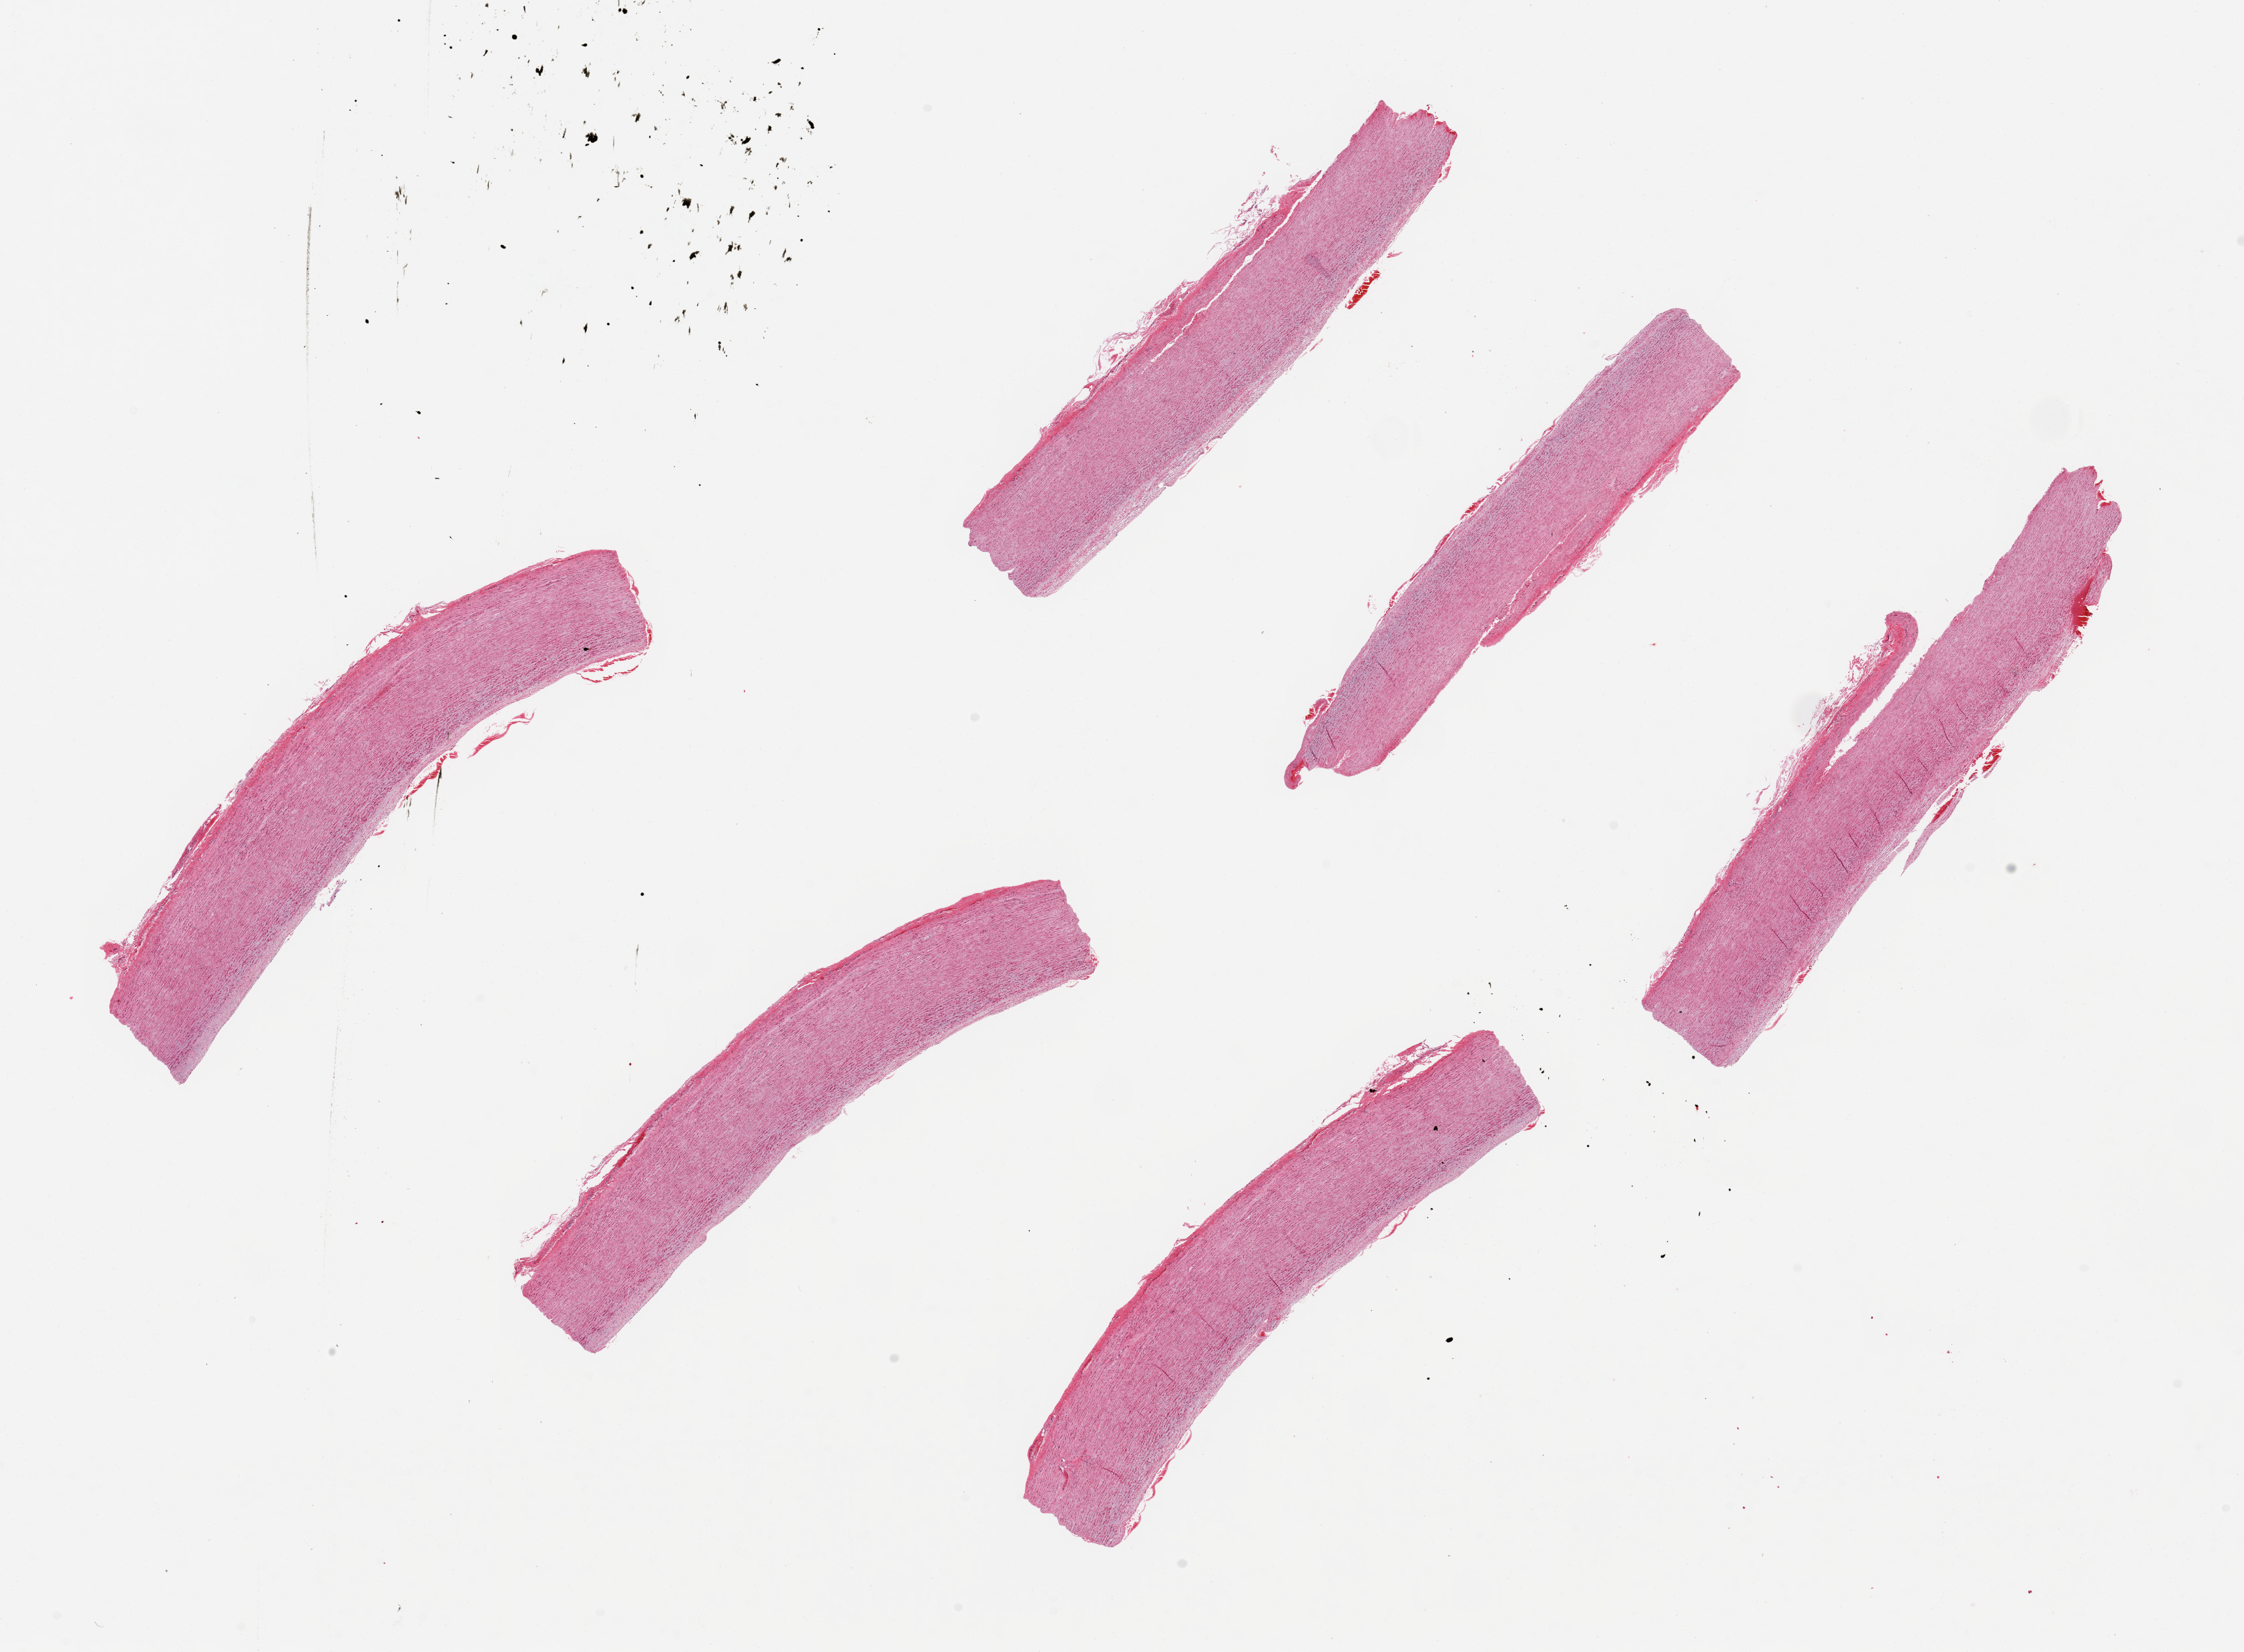
Digitized haematoxylin and eosin-stained section — shown as a low-resolution overview of the whole scanned area (about 26.6 x 19.6 mm, acquisition: 20x scan); PAXgene-fixed, paraffin-embedded tissue; sampled site (target tissue): aorta; donor tissue sample. Donor sex: female.
Review note (as recorded): 6 pieces up to 8x1.5 mm.